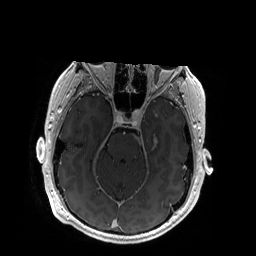
Brain MRI from a brain-tumour surgery series, one axial slice. Position 125 of 192 along the scan axis. T1-weighted post-contrast. 1 mm slice thickness. 256 × 256 image matrix, field of view 256 × 256 mm. Case-level facts recorded for this patient, not image findings: histopathology: Glioblastoma; WHO grade: 4; IDH mutation: no.
Annotated regions visible in this slice (expert manual segmentation):
- tumour: box from (x=135, y=136) to (x=159, y=144) px